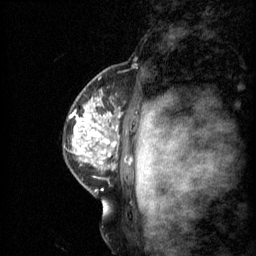
Breast MRI (dynamic contrast-enhanced), one sagittal slice; position 46 of 60 along the scan axis; 3 images stored at this slice position (order not interpretable as contrast timing); 1.5 T; TE 4.2 ms, TR 11 ms; 2 mm slice thickness; 256 × 256 image matrix. Female patient, age 48 years.
Structures marked on this image (semi-automatic segmentation, software-assisted and operator-edited):
- analysis volume of interest (the breast-tissue region the enhancement analysis was run in; not a lesion): bounding box (x1, y1, x2, y2) in pixels: (69, 74, 139, 147)
- tumour enhancement mask (voxels above the 70 % enhancement threshold inside the analysis volume of interest): (70, 100, 120, 147)